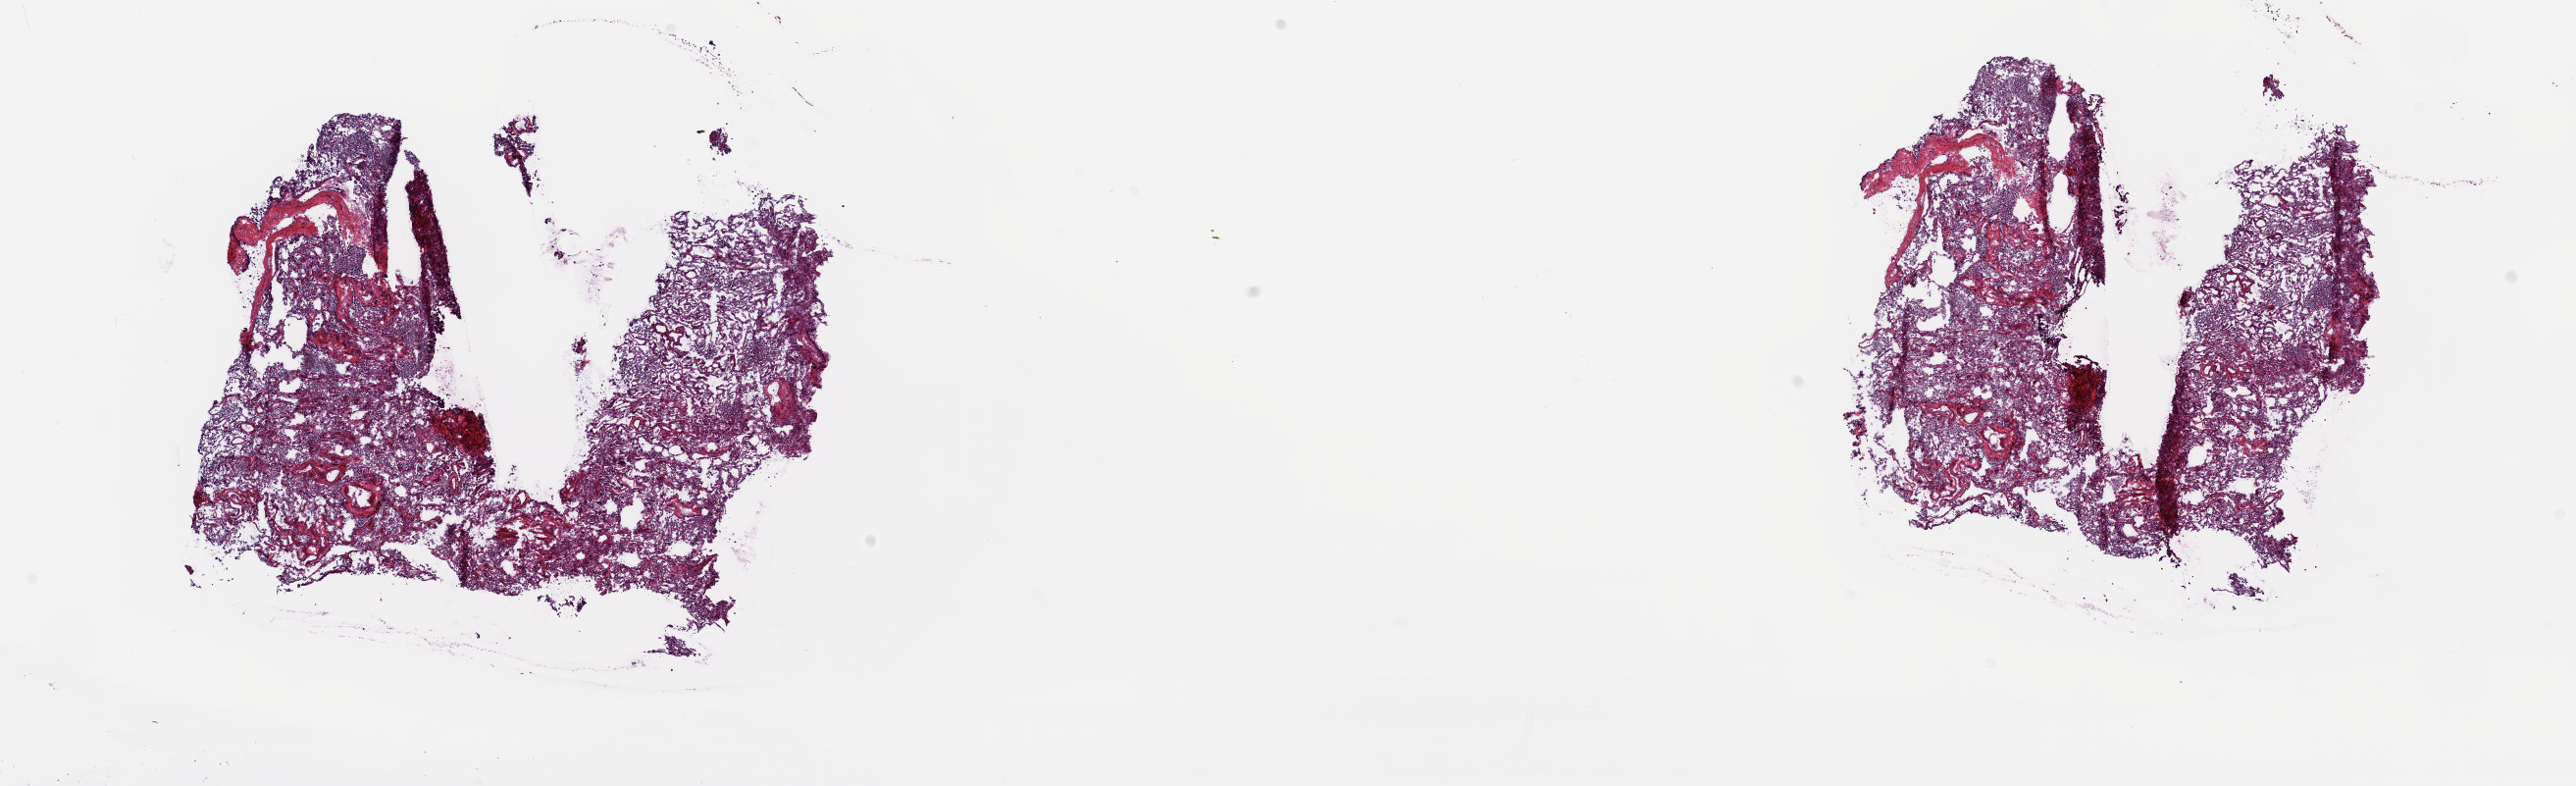
H&E-stained whole-slide image, shown as a low-resolution overview of the whole scanned area (about 20.8 x 6.4 mm). Frozen section. Lung, solid tissue normal (non-tumour tissue) sample. Patient: male, age at initial diagnosis 57 years. Composition of this section per pathologist review: tumour cells 0%, tumour nuclei 0%, normal cells 100%, stromal cells 0%, necrosis 0%. Inflammatory infiltration, as recorded: lymphocyte infiltration 4%, monocyte infiltration 13%, neutrophil infiltration 0%.
This section: solid tissue normal sample (biorepository sample class). Patient diagnosis: Adenocarcinoma, NOS.